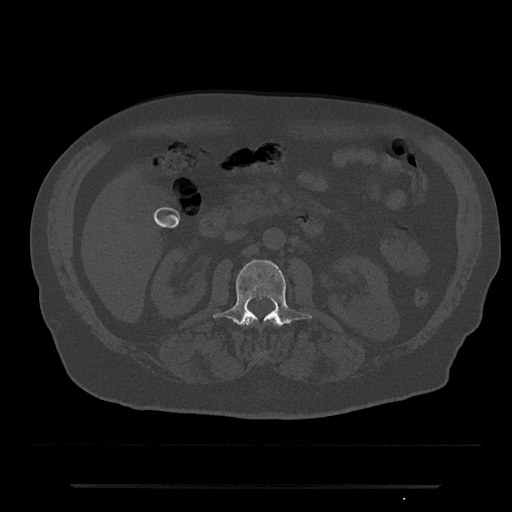
CT including the spine, one axial slice; slice 481 of 797 in the series (ordered by position); bone window (W 1800 / L 400 HU); 0.5 mm slice thickness; 512 × 512 image matrix, field of view 434 × 434 mm. Patient: male, 80 years. Case-level facts recorded for this patient, not image findings: primary cancer: prostate; vertebrae with lytic lesions (as recorded): L1, T11.
Structures marked on this image (semi-automatic segmentation, software-assisted and operator-edited):
- L1 vertebra: bounding box [x1, y1, x2, y2] px = [243, 319, 279, 326]
- L2 vertebra: [213, 260, 312, 326]